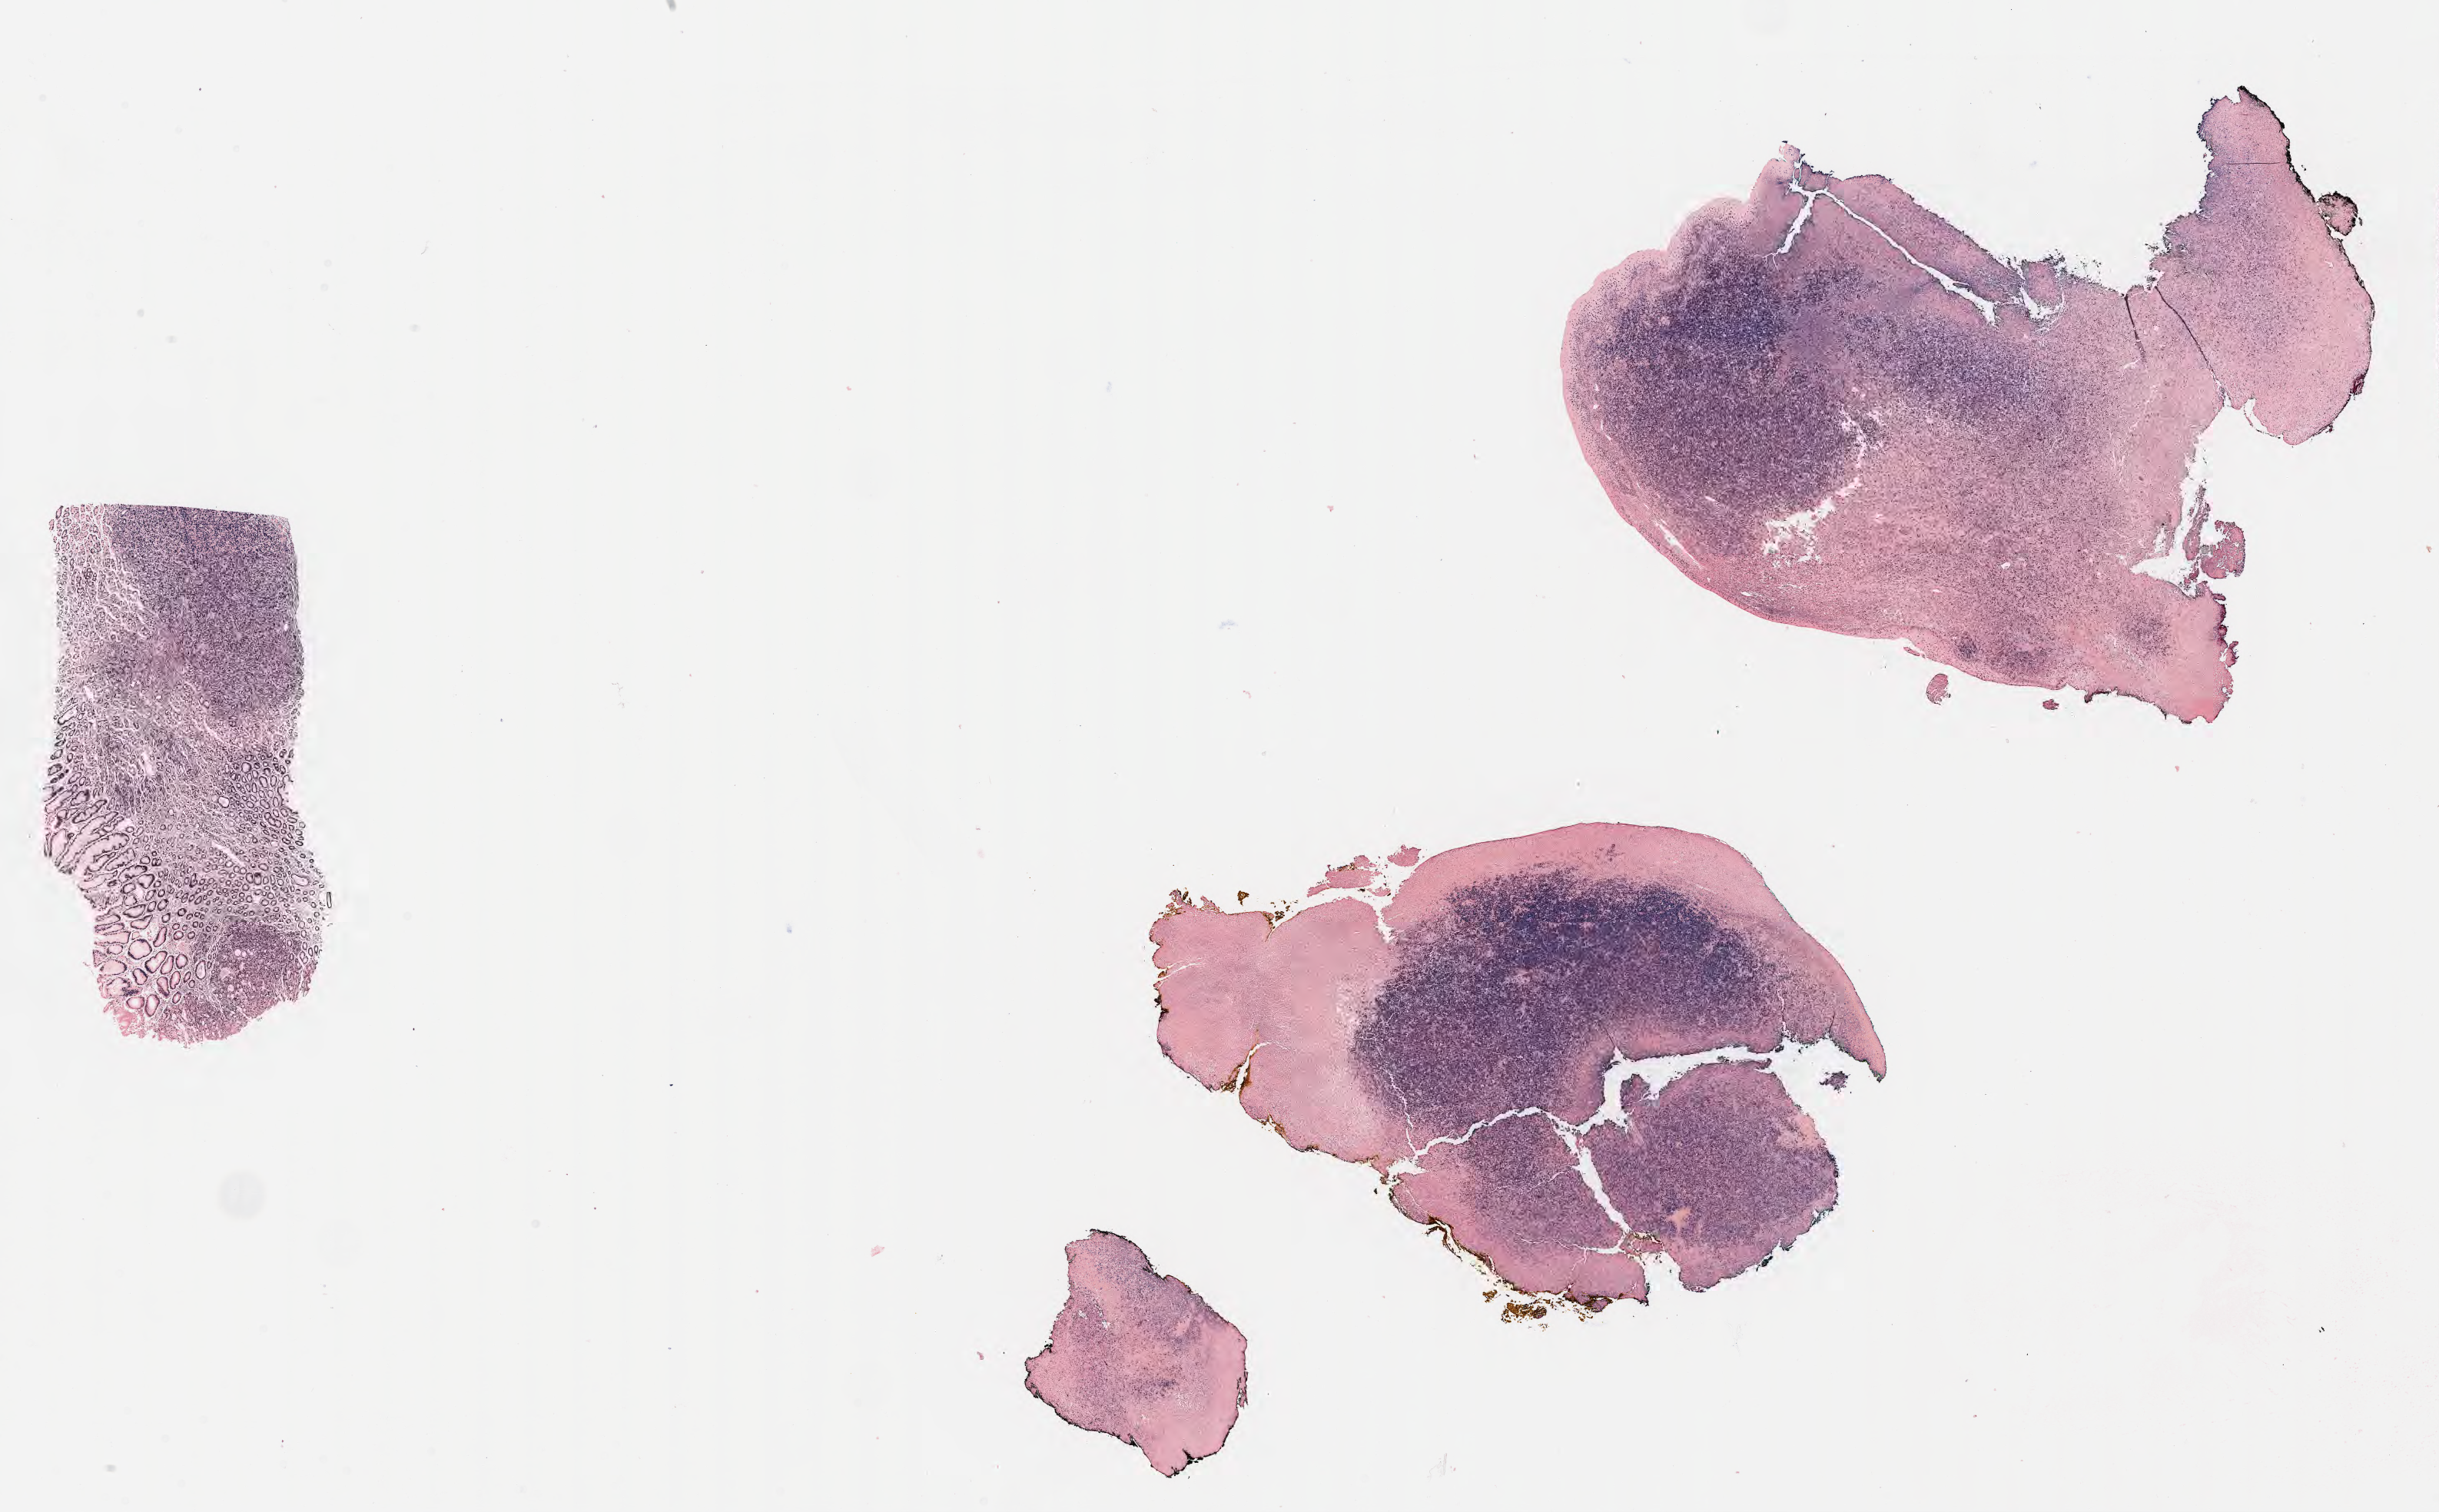
Whole-slide image; stain recorded as Iodonitrotetrazolium — low-resolution overview of the scanned area, about 25.7 x 15.9 mm; tumor tissue. Patient: male, age 49 years.
Diagnosis: Diffuse large B-cell lymphoma, NOS.